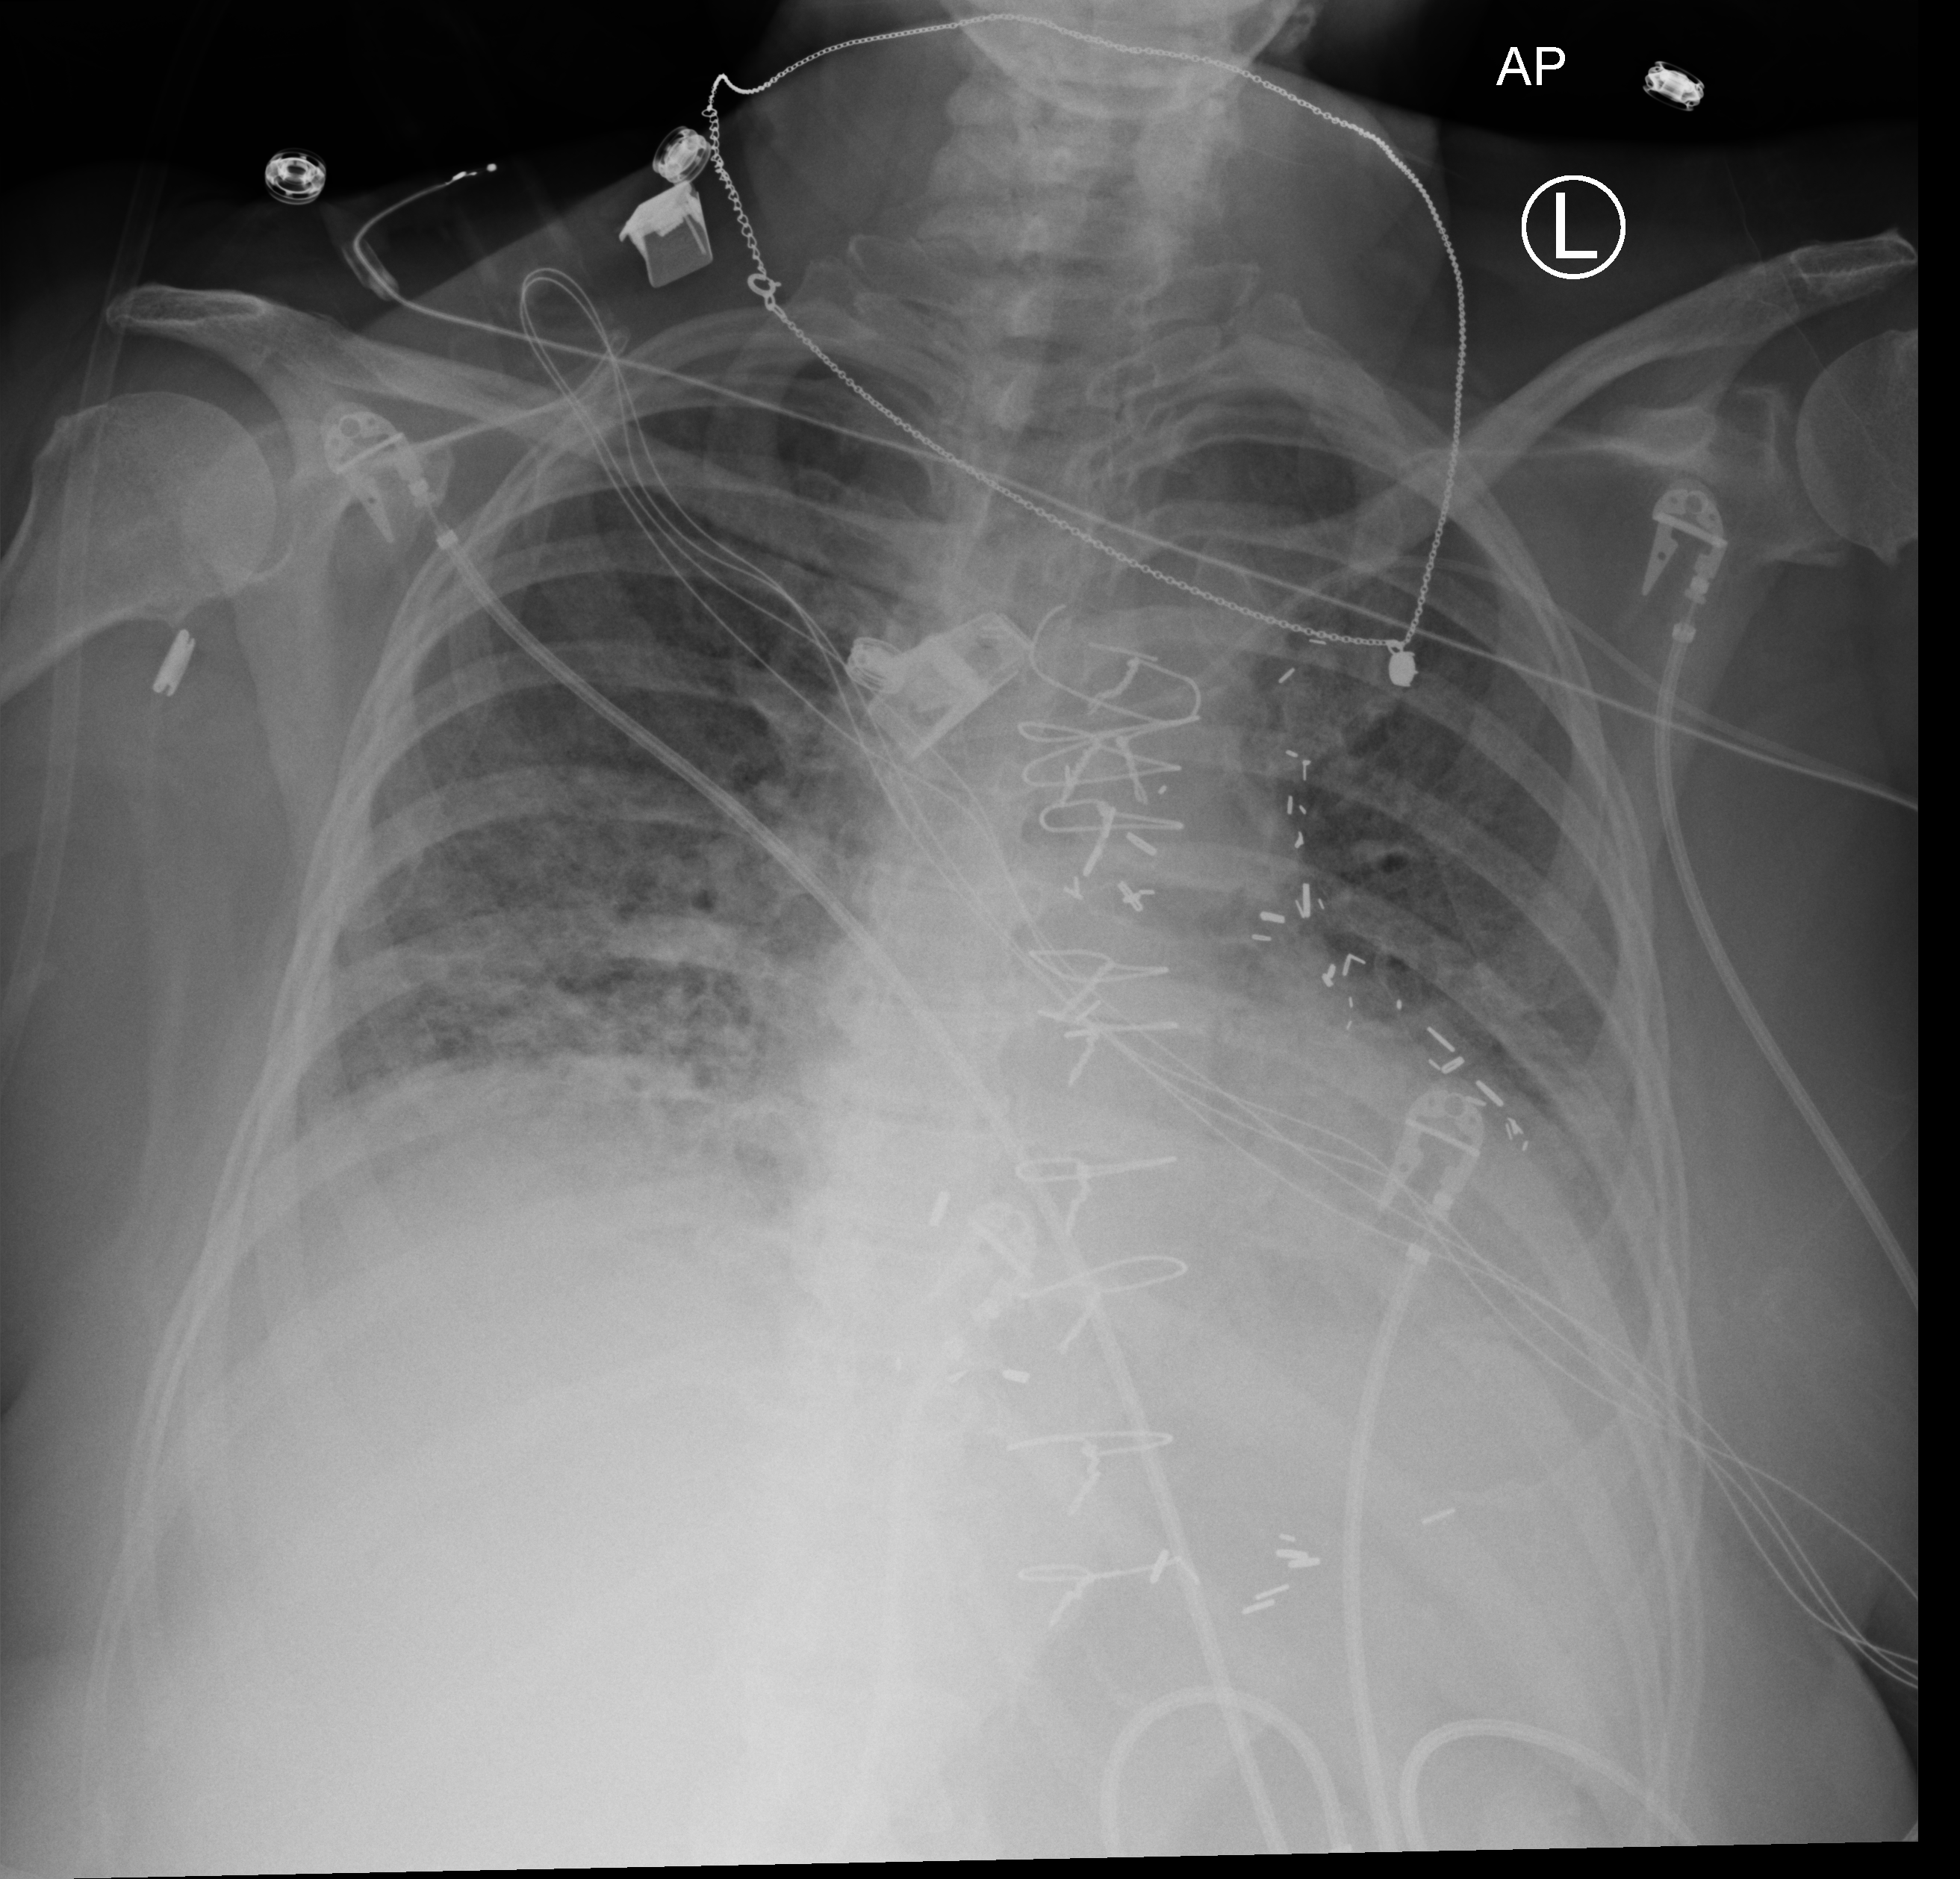
Chest X-ray (portable). Female patient hospitalised with COVID-19, age 60–74 years.
Hospital-stay facts (about this admission, not read from this image; timing relative to this image not recorded): hypertension (admission record): yes; COPD (admission record): no.